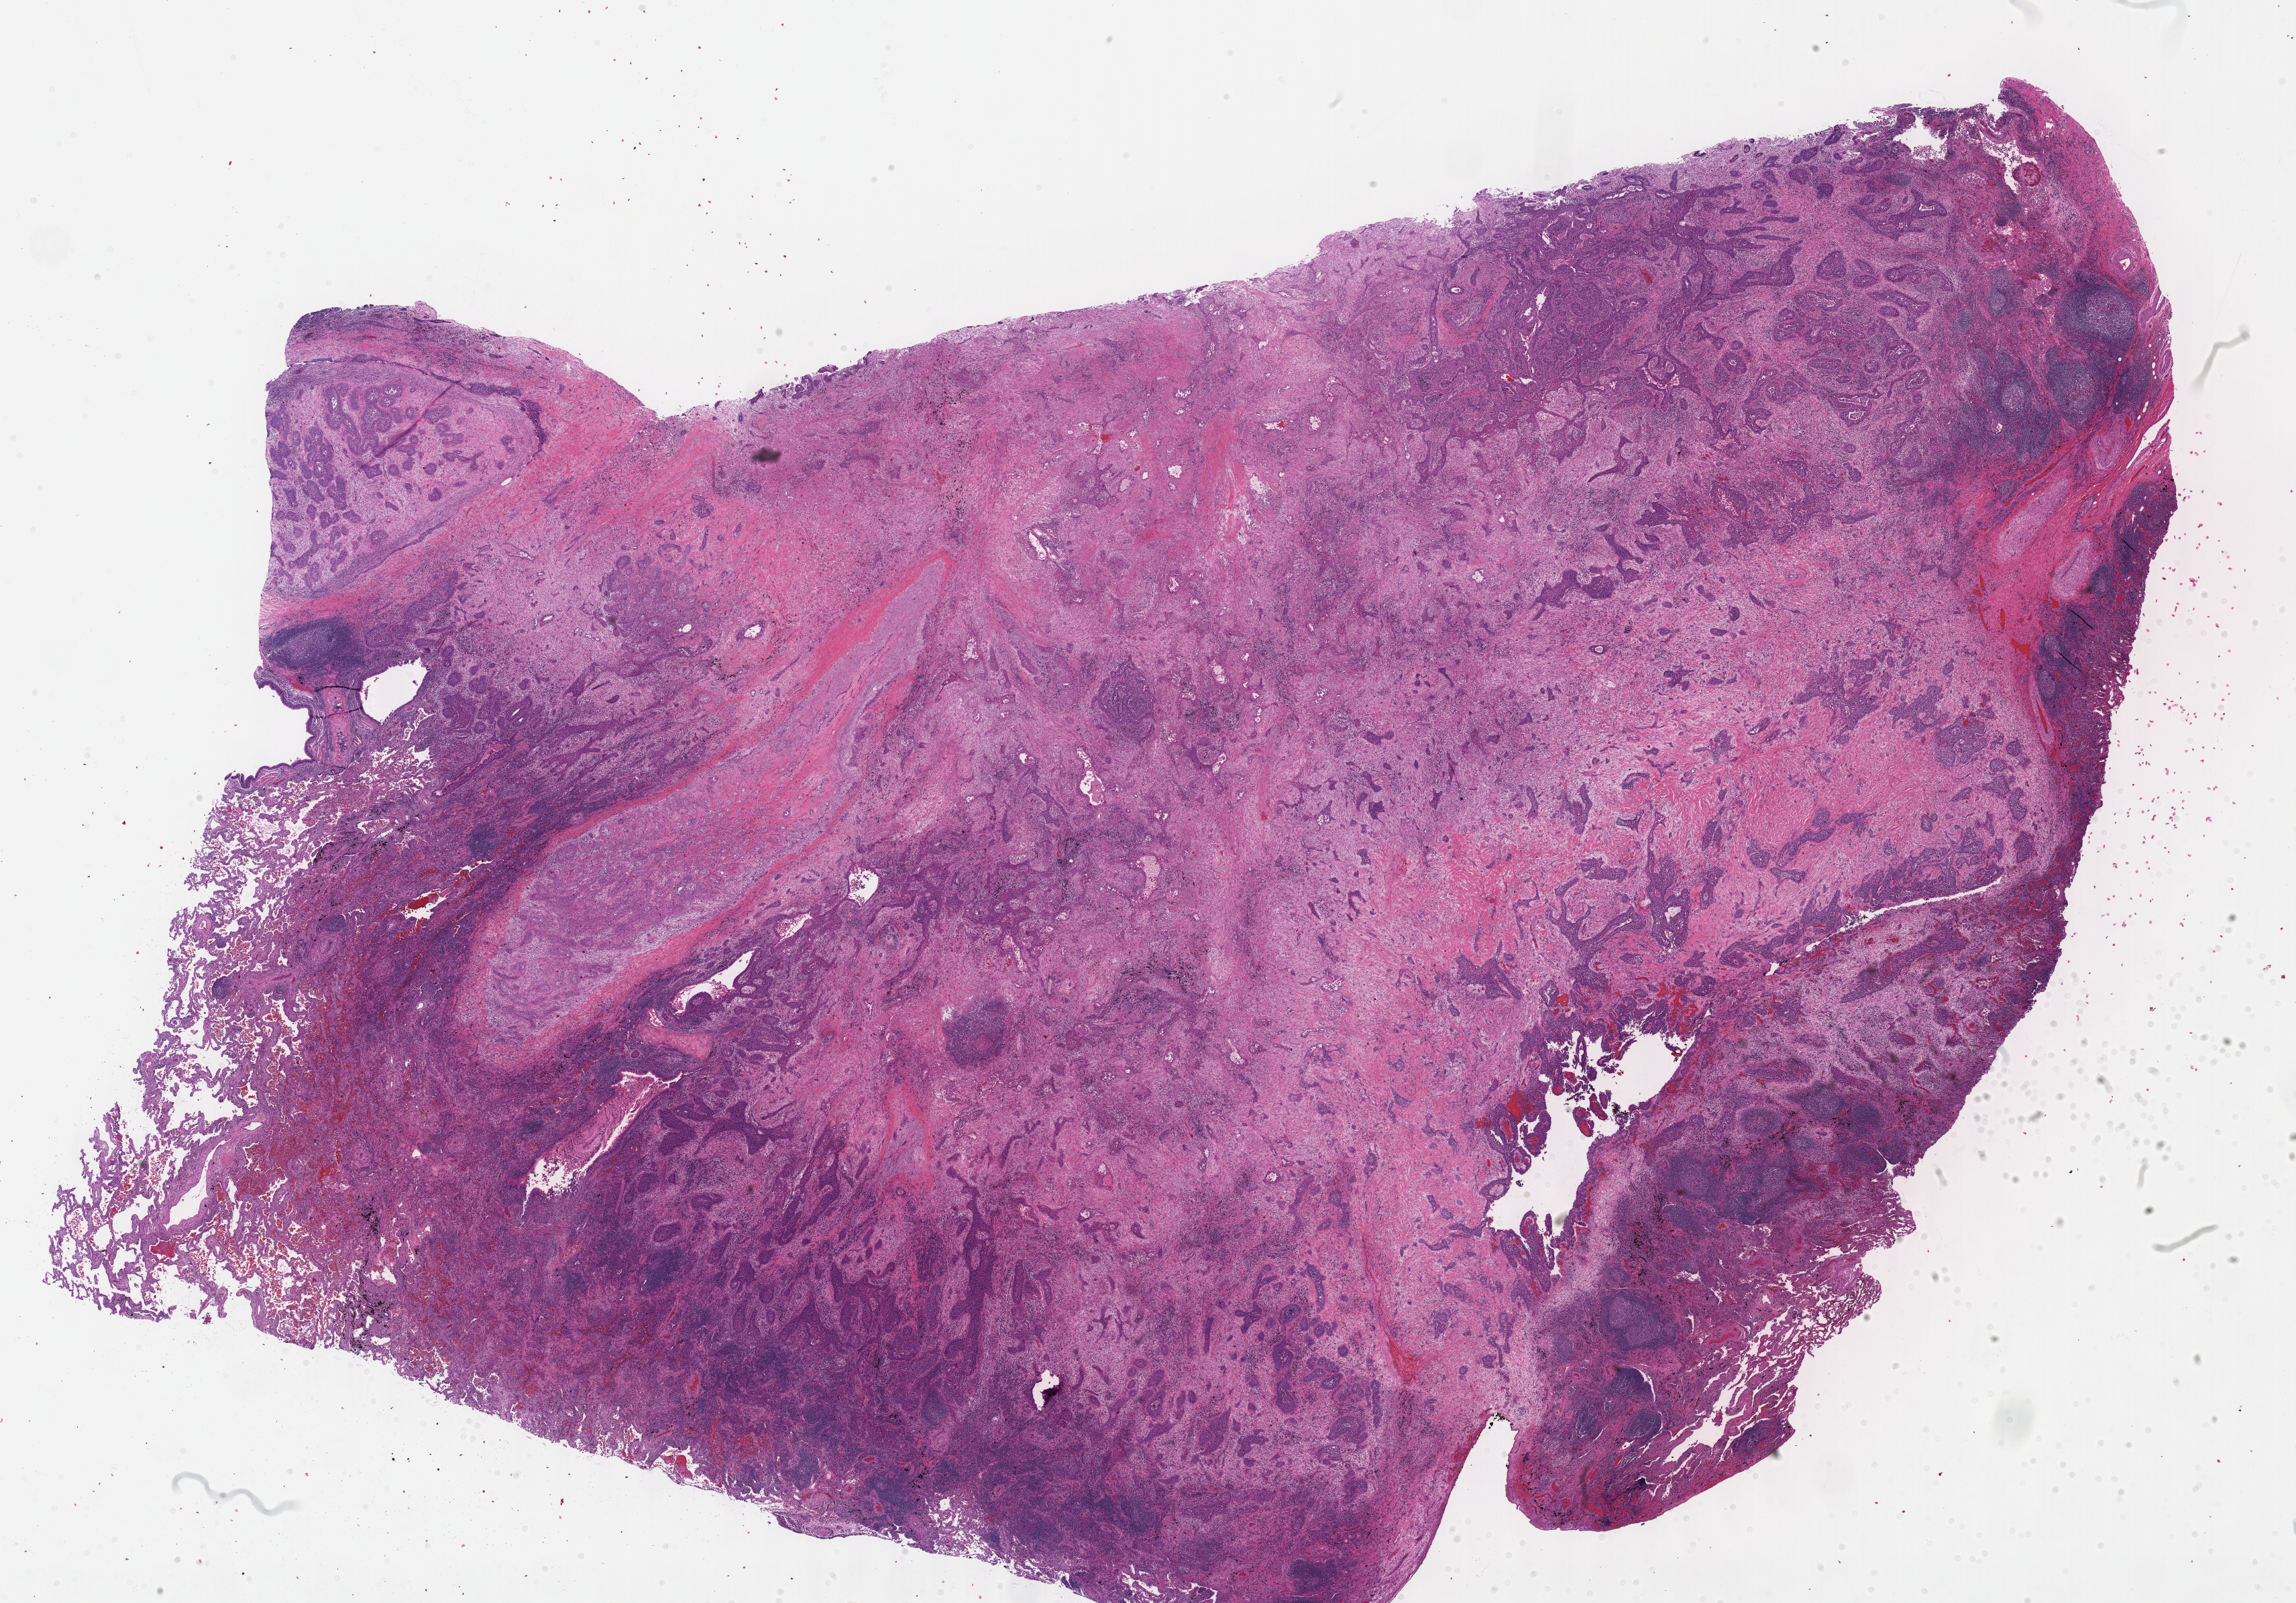
H&E-stained whole-slide image, whole scanned area (about 27.7 x 19.3 mm, slide scanned at 40x) shown as a low-resolution overview. Formalin-fixed paraffin-embedded (FFPE) diagnostic section. Sample: primary tumour, lung. Female, age 65 years at initial diagnosis.
Diagnosis: Squamous cell carcinoma, NOS (upper lobe, lung). AJCC pathologic stage: IIB (6th edition).